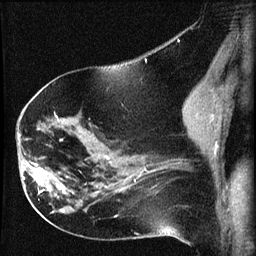
Breast MRI (dynamic contrast-enhanced), one sagittal slice; slice 34 of 60 in the series (ordered by position); dynamic contrast-enhanced series, image 2 of 3 at this slice position (ordered by acquisition); 1.5 T; TE 4.2 ms, TR 8.2 ms; 2 mm slice thickness; 256 × 256 image matrix, field of view 180 × 180 mm. Patient: female, 63 years.
Structures marked on this image (semi-automatic segmentation, software-assisted and operator-edited):
- analysis volume of interest (the breast-tissue region the enhancement analysis was run in; not a lesion): bounding box [x1, y1, x2, y2] px = [22, 156, 64, 202]
- tumour enhancement mask (voxels above the 70 % enhancement threshold inside the analysis volume of interest): [23, 164, 64, 193]